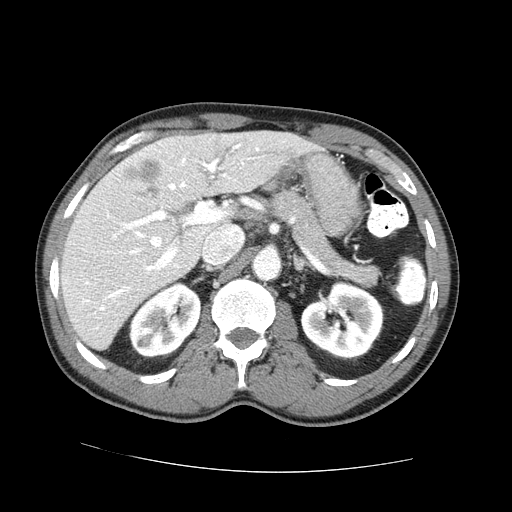
Contrast-enhanced abdominal CT (liver protocol), one axial slice; slice 42 of 73 in the series (ordered by position); reconstruction kernel STANDARD; 100 kVp; one of 2 acquisitions stored at this slice position; soft-tissue window (W 400 / L 40 HU); 2.5 mm slice thickness; 512 × 512 image matrix, field of view 380 × 380 mm. Case-level facts recorded for this patient, not image findings: diagnosis: hepatocellular carcinoma (patient treated with transarterial chemoembolisation; whether this scan precedes or follows treatment is not stated here); TNM stage (as recorded): Stage-IVA; Child-Pugh class: A; tumour nodularity: uninodular.
Annotated regions visible in this slice (semi-automatic segmentation, software-assisted and operator-edited):
- liver parenchyma outside the tumour (the mass and vessels are separate outlines, so this box may not span the whole liver): bounding box [x1, y1, x2, y2] px = [60, 132, 314, 350]
- mass: [124, 159, 162, 199]
- liver vessels: [82, 142, 259, 311]